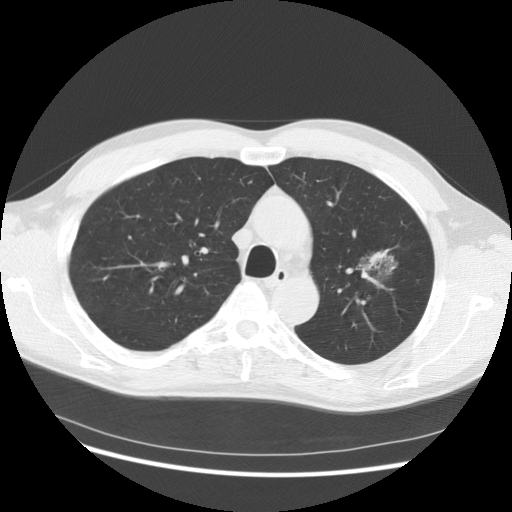
Low-dose screening chest CT, axial slice. Third screening round (two years after baseline). Lung window (W 1500 / L -600 HU). Standard (soft-tissue) reconstruction kernel (STANDARD). 140 kVp. Slice 100 of 145 in the series. Male, age 61 years at enrolment. Former smoker at enrolment.
Expert-annotated lung lesion, bounding box <332,226,414,307> (left, top, right, bottom; pixels). The exam's reader record, not a measurement of the box and not confirmed to be the same lesion: non-calcified nodule or mass ≥4 mm, left upper lobe, 37 × 33 mm, poorly defined margins, mixed attenuation, pre-existing on the prior screen: yes; interval growth: yes. Lung cancer was diagnosed 361 days after this screen: bronchiolo-alveolar adenocarcinoma, NOS, left upper lobe, well differentiated (G1), stage IB (AJCC 6th edition), 44 mm at pathology.